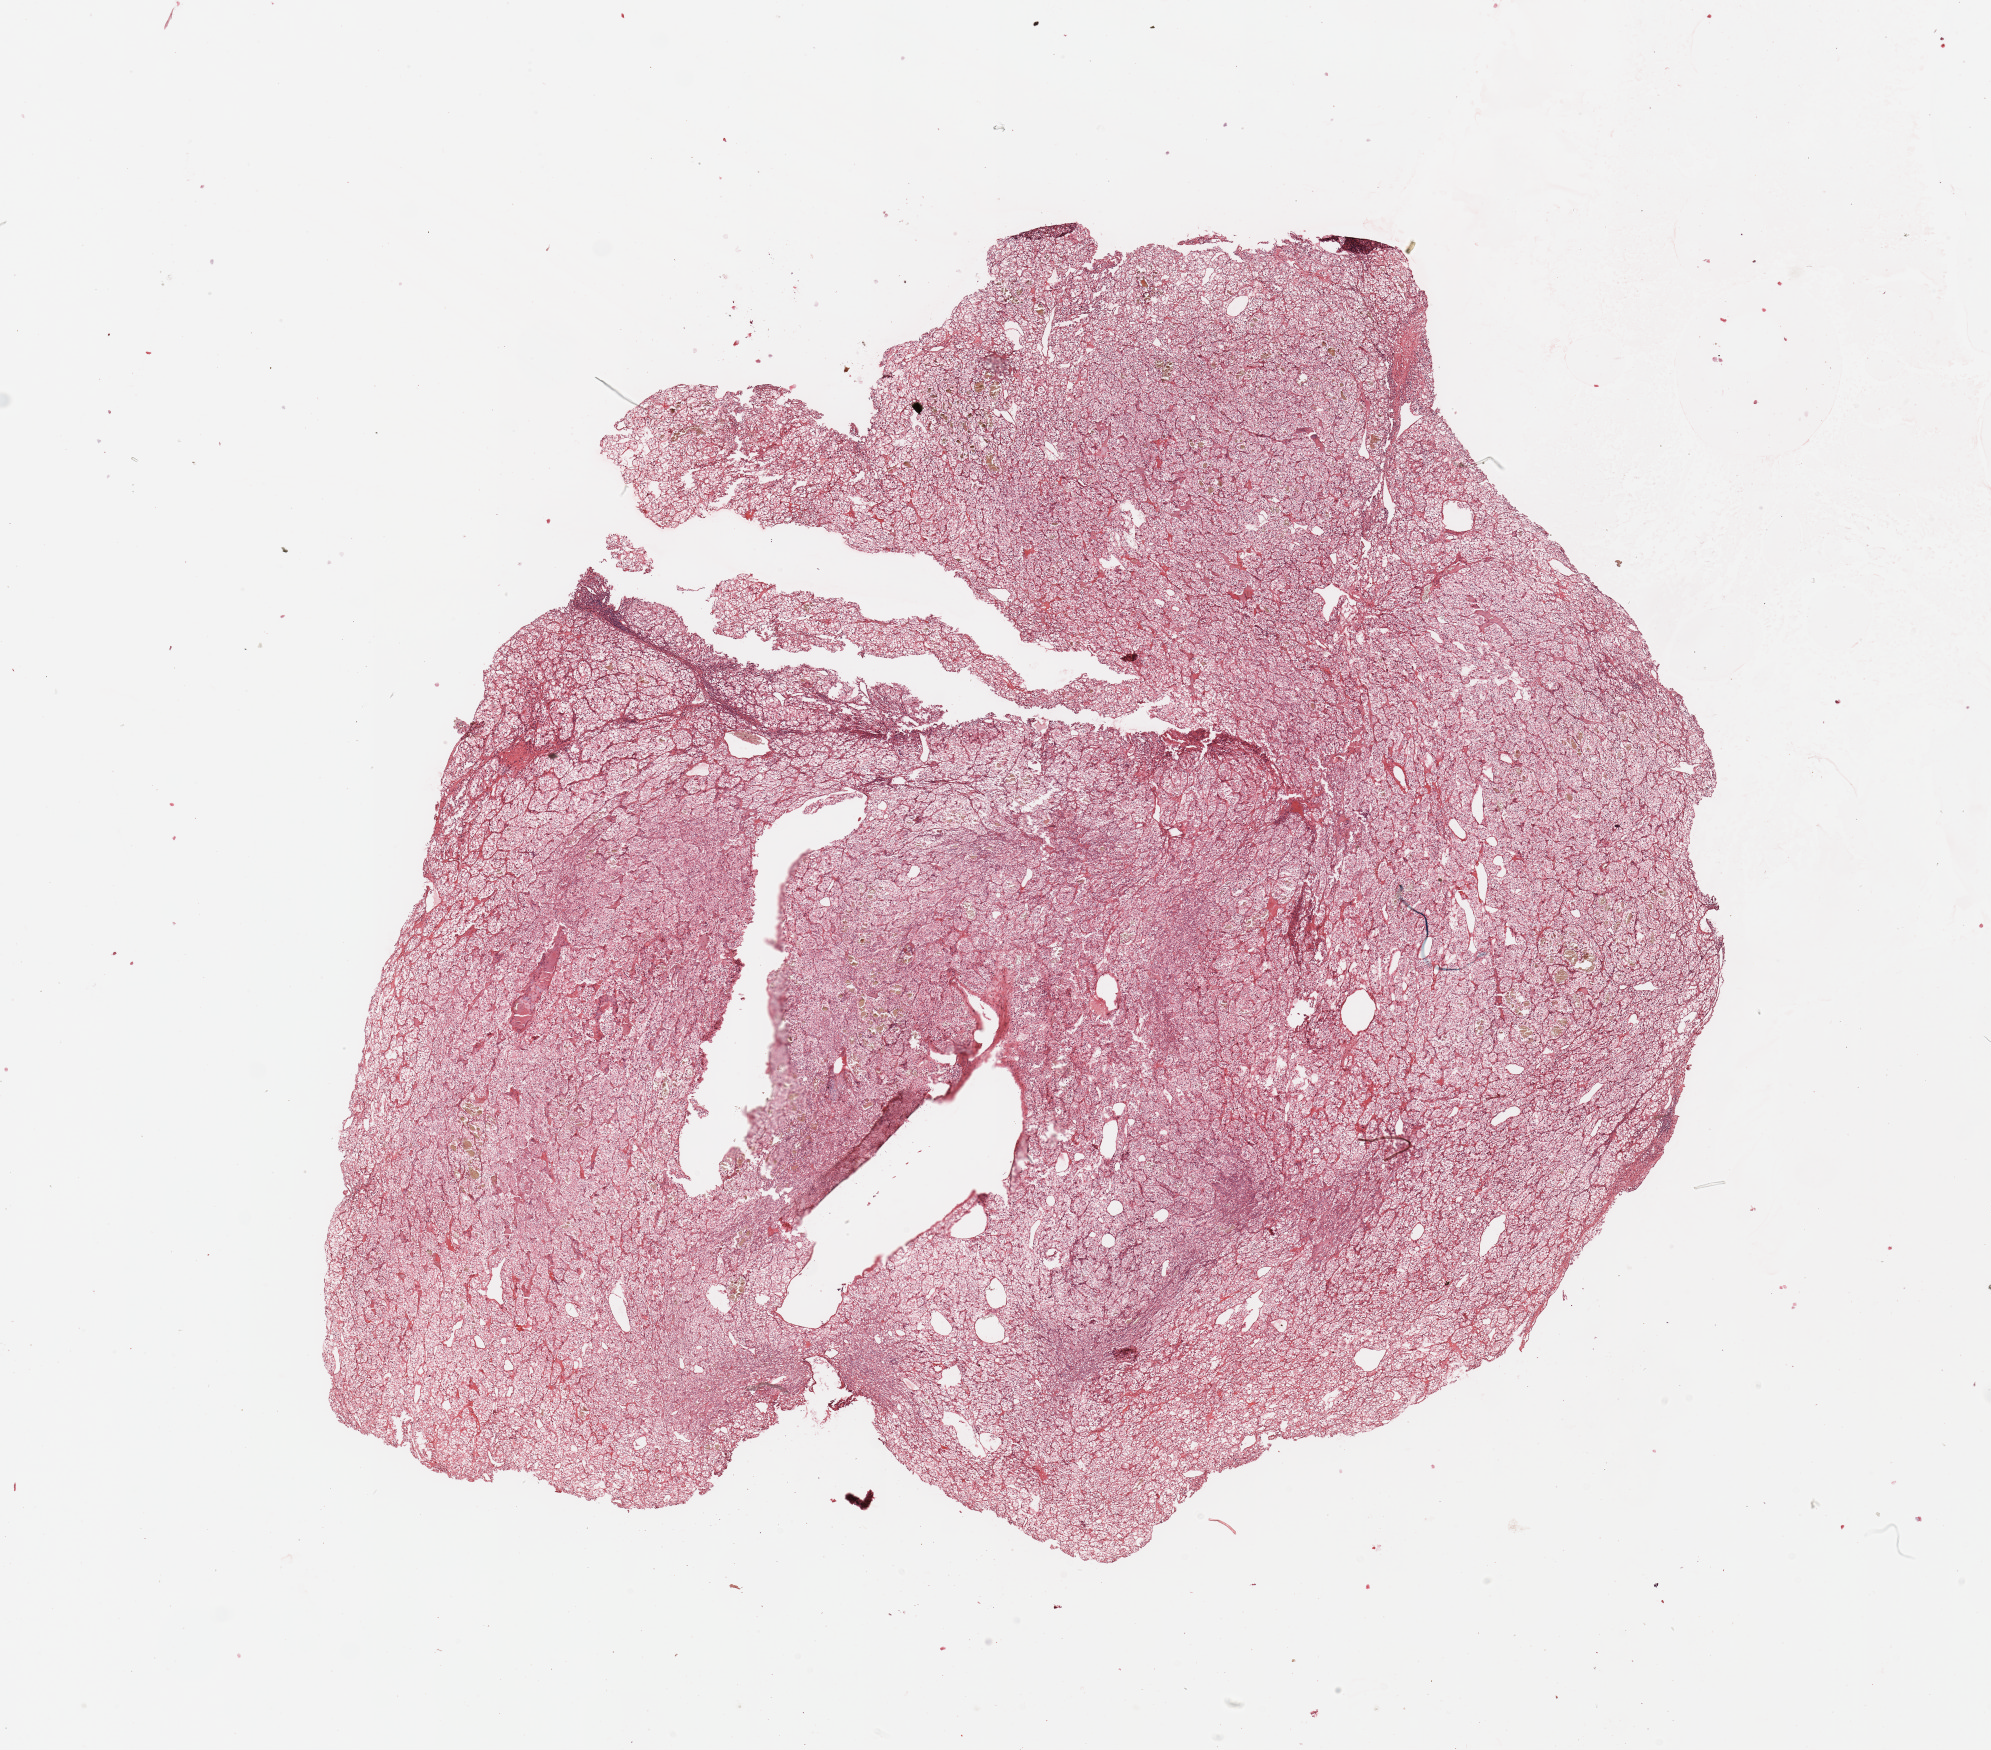
Digitized Hematoxylin and eosin (H&E) stained tissue section (whole slide) — a low-resolution overview of the entire scanned area, about 15.8 x 13.8 mm (slide scanned at 20x), tumour tissue sample, kidney. Patient: male, age 65 years. Histologic grade: G2 (moderately differentiated).
Primary tumour site (as recorded): upper pole. AJCC pathologic stage: III. Histologic diagnosis: Renal cell carcinoma, NOS.